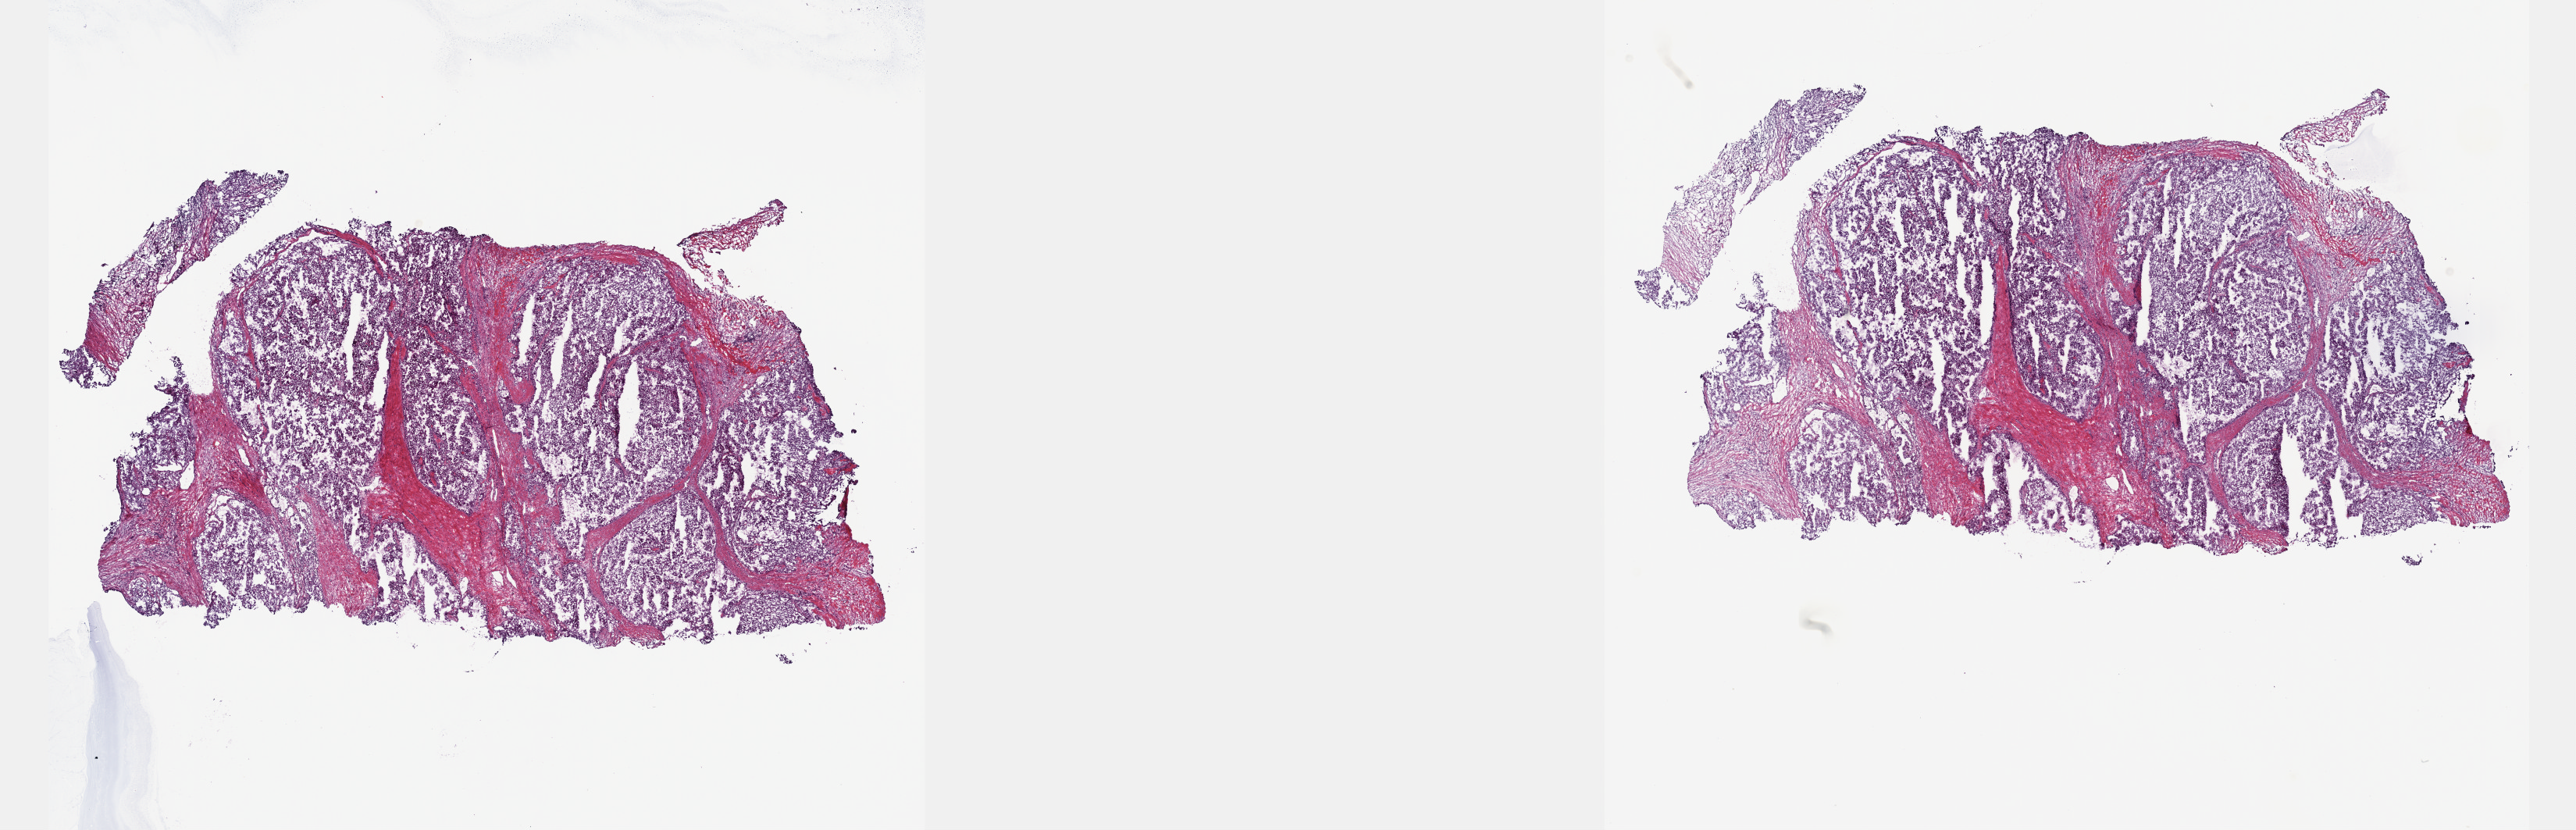
Digitized H&E tissue section (whole slide) — shown as a low-resolution overview of the whole scanned area (about 26.7 x 8.6 mm, slide scanned at 40x); frozen section from the top of the tissue portion; sample: primary tumour, kidney. Male, age 50 years at initial diagnosis. Pathologist review of this section (percent, as recorded): tumour cells 70%, tumour nuclei 70%, normal cells 0%, stromal cells 30%, necrosis 0%. Inflammatory infiltration, as recorded: lymphocyte infiltration 0%, monocyte infiltration 5%, neutrophil infiltration 0%.
AJCC pathologic stage: III. Pathologic diagnosis: Papillary adenocarcinoma, NOS.